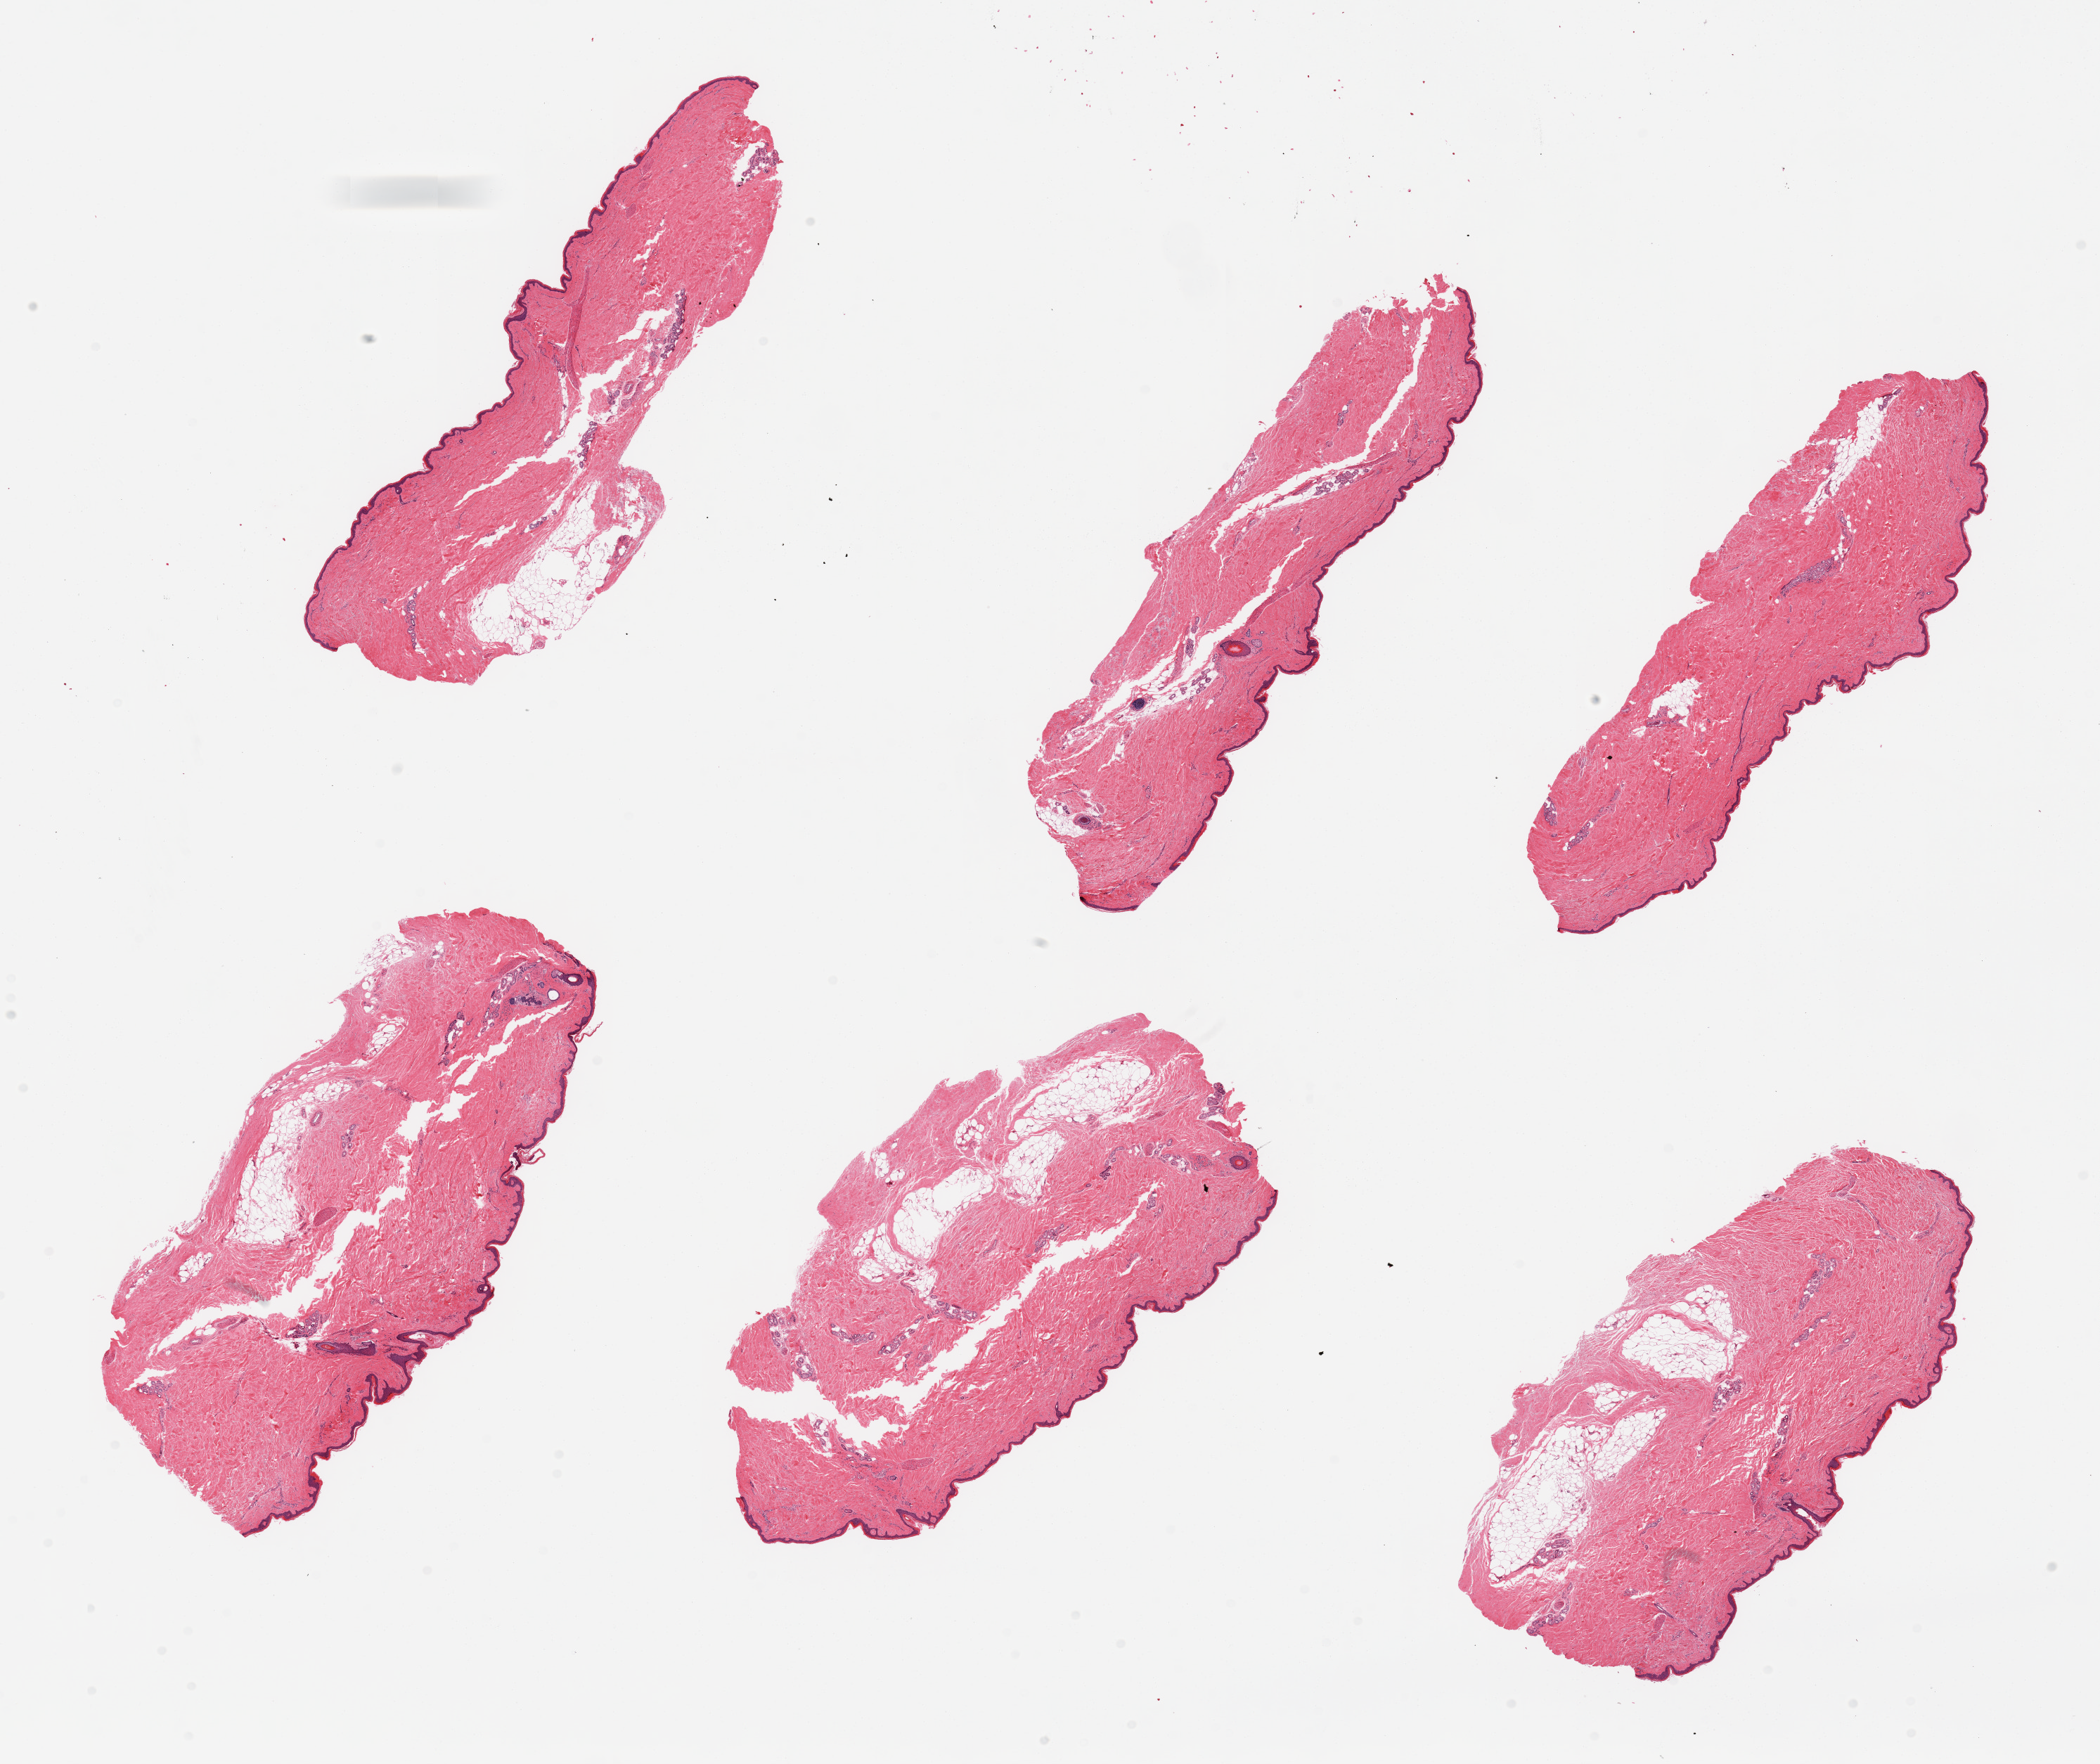
Digitized haematoxylin and eosin-stained section, low-resolution overview of the scanned area, about 23.6 x 19.8 mm, PAXgene-fixed paraffin-embedded (PFPE) section, target tissue: skin of lower leg, tissue donor sample. Male donor.
• reviewer comment on this tissue sample: 6 pieces, minimal dermal fat; squamous epithelium is ~40 microns